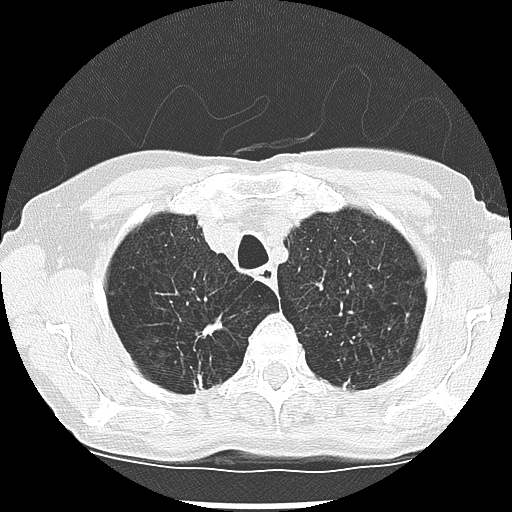
Low-dose screening chest CT, one axial slice; slice 227 of 265 in the series (ordered by position); reconstruction kernel LUNG; 120 kVp; lung window (W 1500 / L -600 HU); 2.5 mm slice thickness; 512 × 512 image matrix.
Structures marked on this image (outlined manually by an expert reader):
- lesion 1 (nodule, upper lobe of right lung): bounding box [x1, y1, x2, y2] px = [196, 376, 202, 390]
- lesion 2 (tumor, upper lobe of right lung): [204, 322, 220, 334]